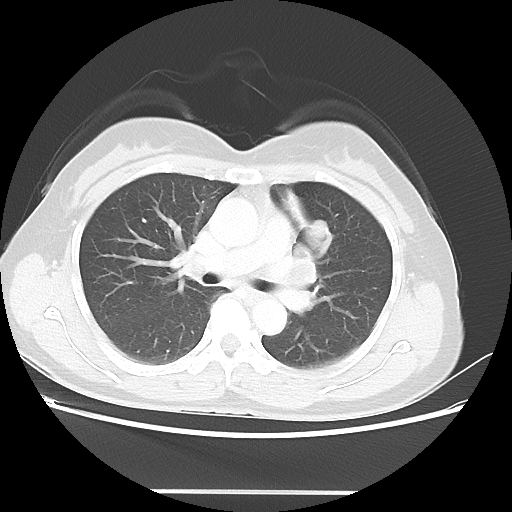
Chest CT, one axial slice; reconstruction kernel LUNG; lung window (W 1500 / L -600 HU); 5 mm slice thickness; 512 × 512 image matrix, field of view 360 × 360 mm. Patient: female, 50 years. From the clinical record (not read from this slice): clinical TNM (as recorded): T1c N1 M0; histopathological grade: G3.
Outlined on this slice (bounding box drawn by a radiologist):
- lung tumour (recorded histology: adenocarcinoma): box from (x=308, y=214) to (x=331, y=243) px